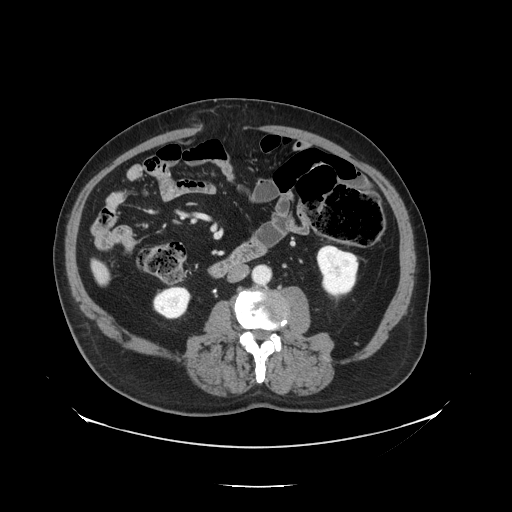
Contrast-enhanced abdominal CT, one axial slice; slice 31 of 138 in the series (ordered by position); 120 kVp; intravenous contrast given; soft-tissue window (W 400 / L 40 HU); 512 × 512 image matrix. Male patient, age 77 years. Case-level facts recorded for this patient, not image findings: diagnosis: colorectal cancer liver metastases, imaged before liver resection; multiple liver metastases: no; largest metastasis: 1.5 cm.
Outlined on this slice (expert manual segmentation):
- liver: bounding box <94,263,110,283> (left, top, right, bottom; pixels)
- planned liver remnant (the part of the liver to remain after resection): <94,263,106,273>